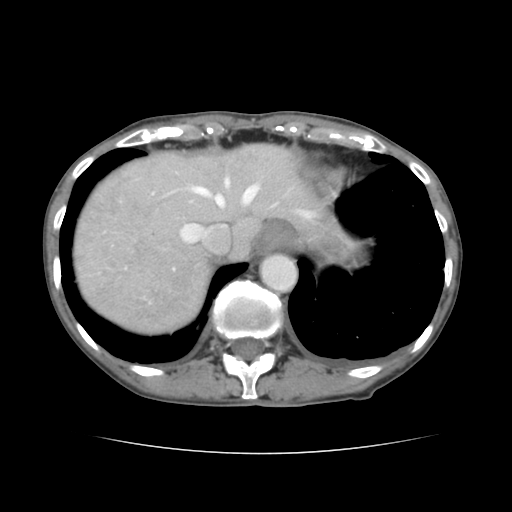
Contrast-enhanced abdominal CT, one axial slice; slice 119 of 136 in the series (ordered by position); intravenous contrast given; soft-tissue window (W 400 / L 40 HU); 512 × 512 image matrix, field of view 319 × 319 mm. Female patient, age 77 years. Case-level facts recorded for this patient, not image findings: diagnosis: colorectal cancer liver metastases, imaged before liver resection; multiple liver metastases: yes; largest metastasis: 3 cm; disease in both lobes: no.
Outlined on this slice (manually delineated by an expert):
- hepatic veins: box from (x=137, y=177) to (x=309, y=244) px
- liver: (x=75, y=145)–(x=331, y=332)
- planned liver remnant (the part of the liver to remain after resection): (x=175, y=145)–(x=332, y=256)